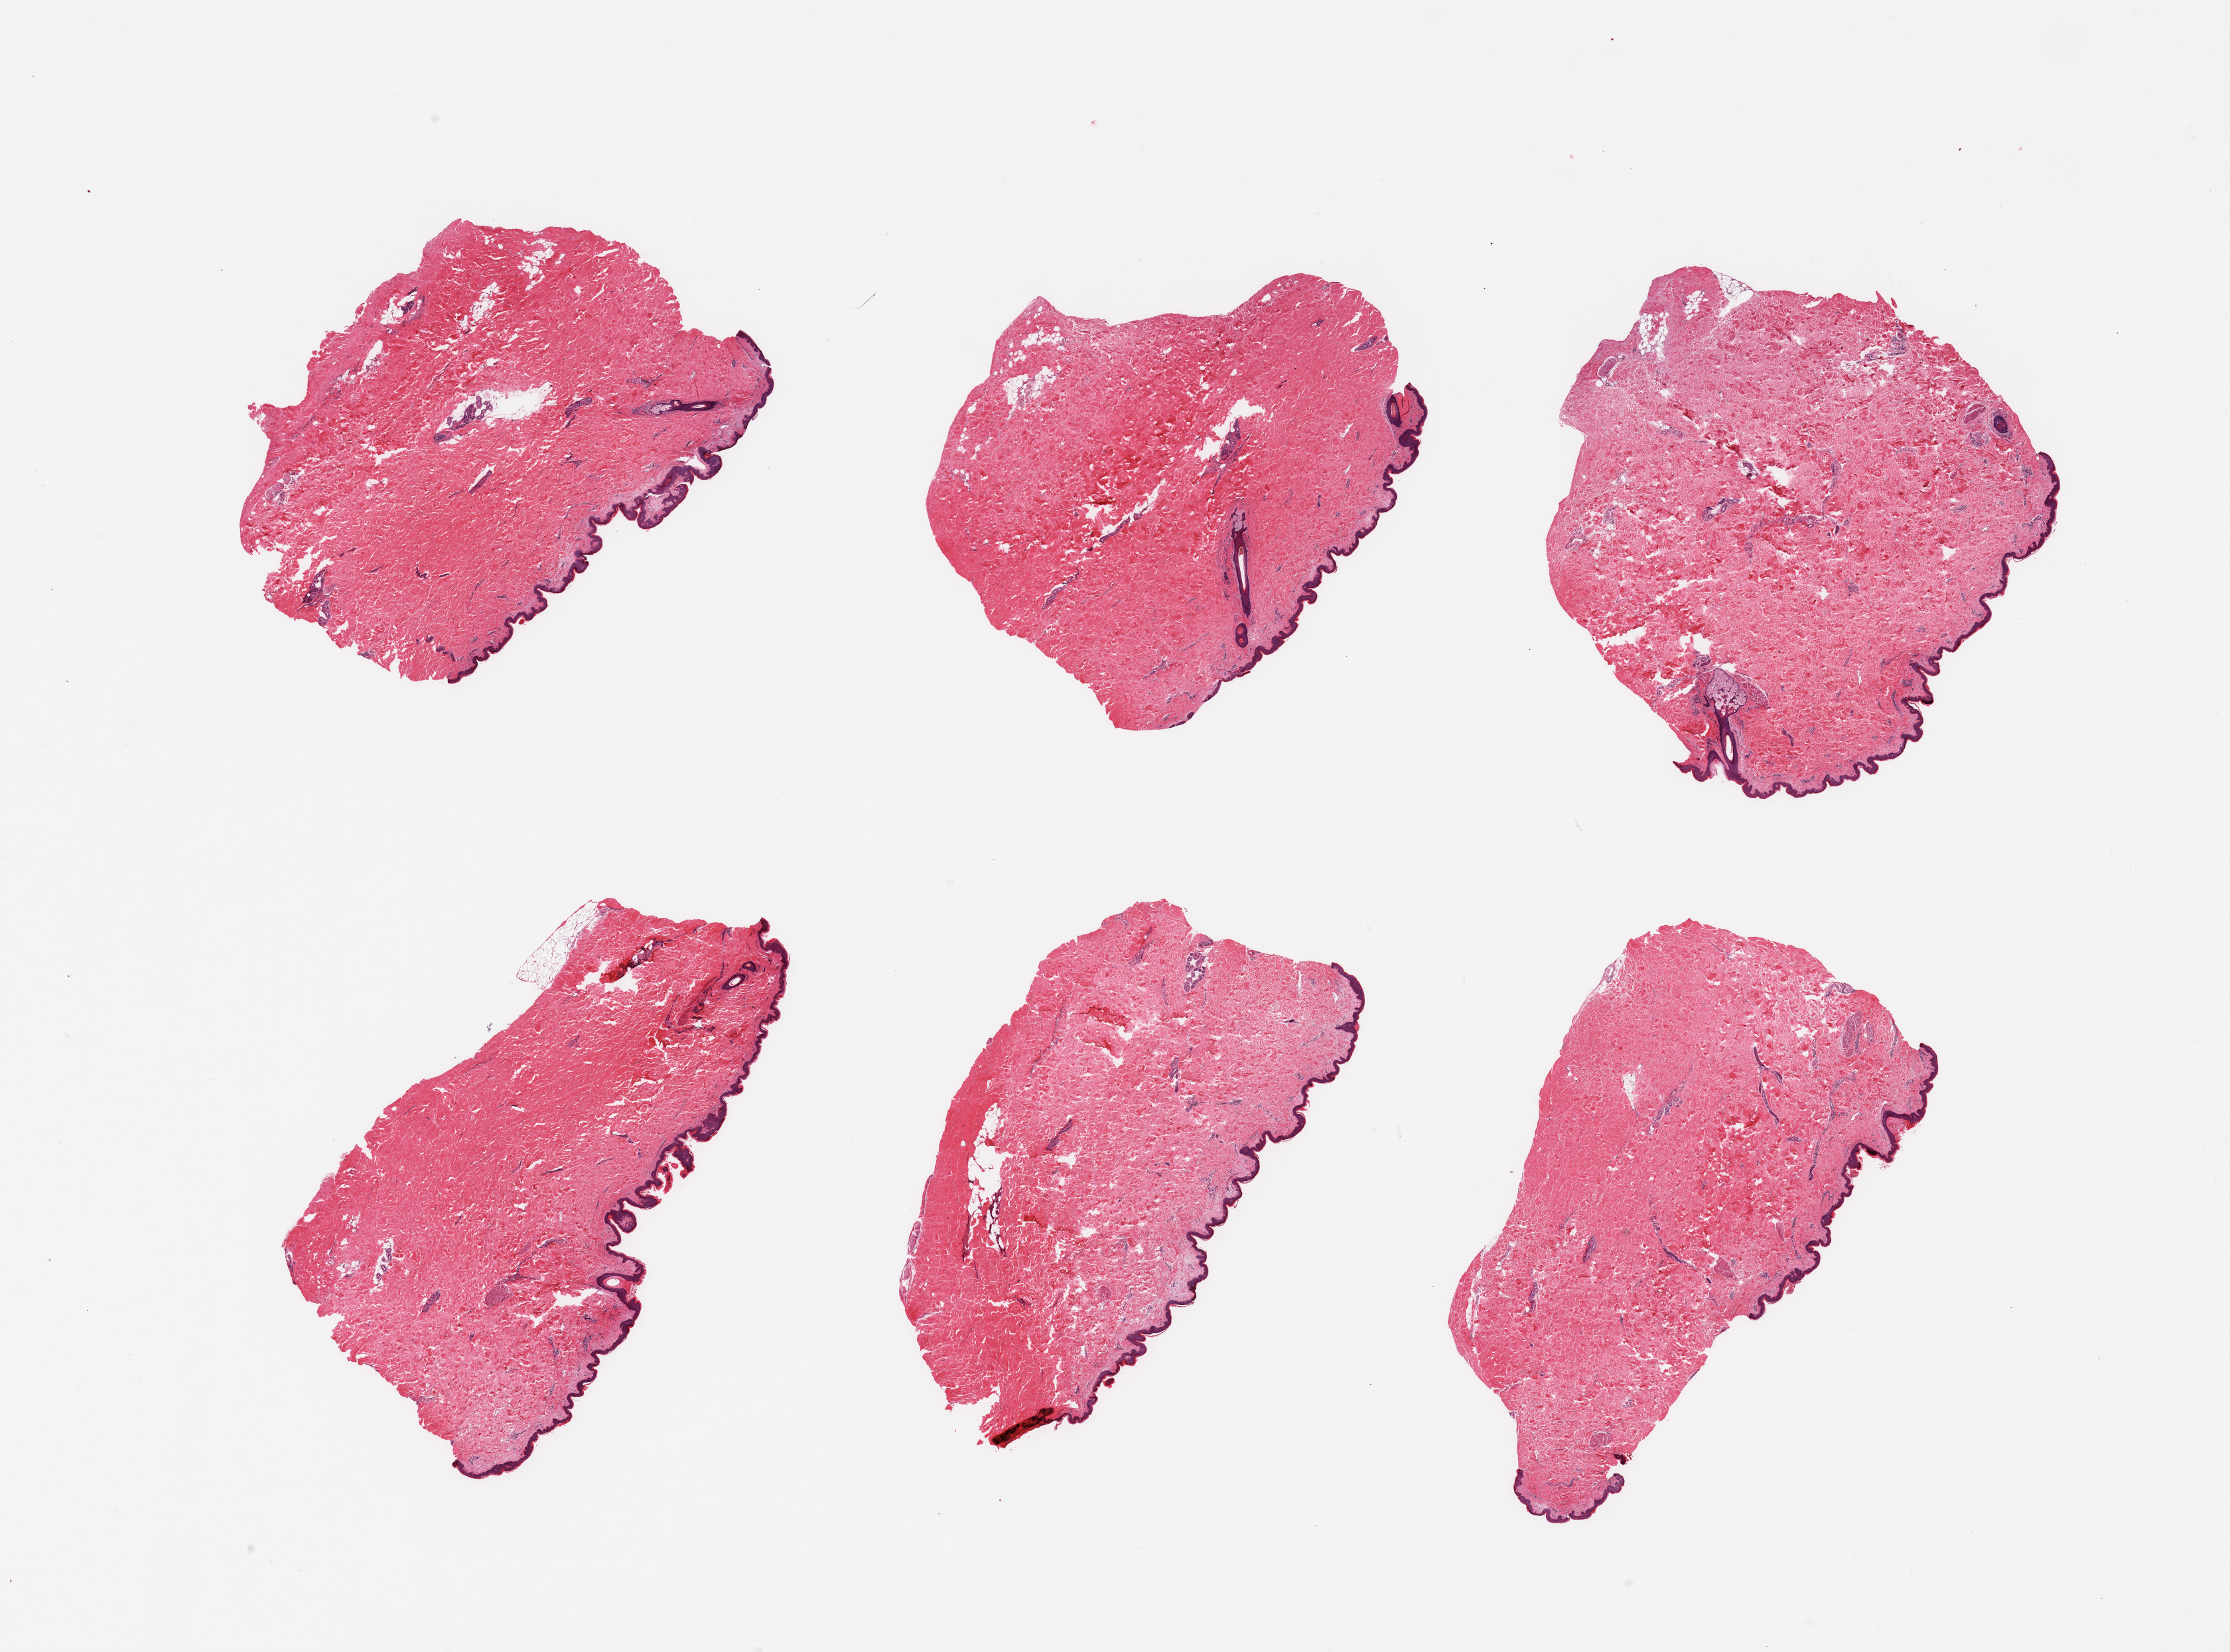
Whole-slide image, H&E stain, brightfield — low-resolution overview of the scanned area, about 26.6 x 19.7 mm (from a 20x scan); PAXgene-fixed paraffin-embedded (PFPE) section; section of skin of suprapubic region (target tissue); tissue donor sample. Male donor.
Review note (as recorded): 6 pieces; well trimmed; a few hair follicles; 5% dermal fat.